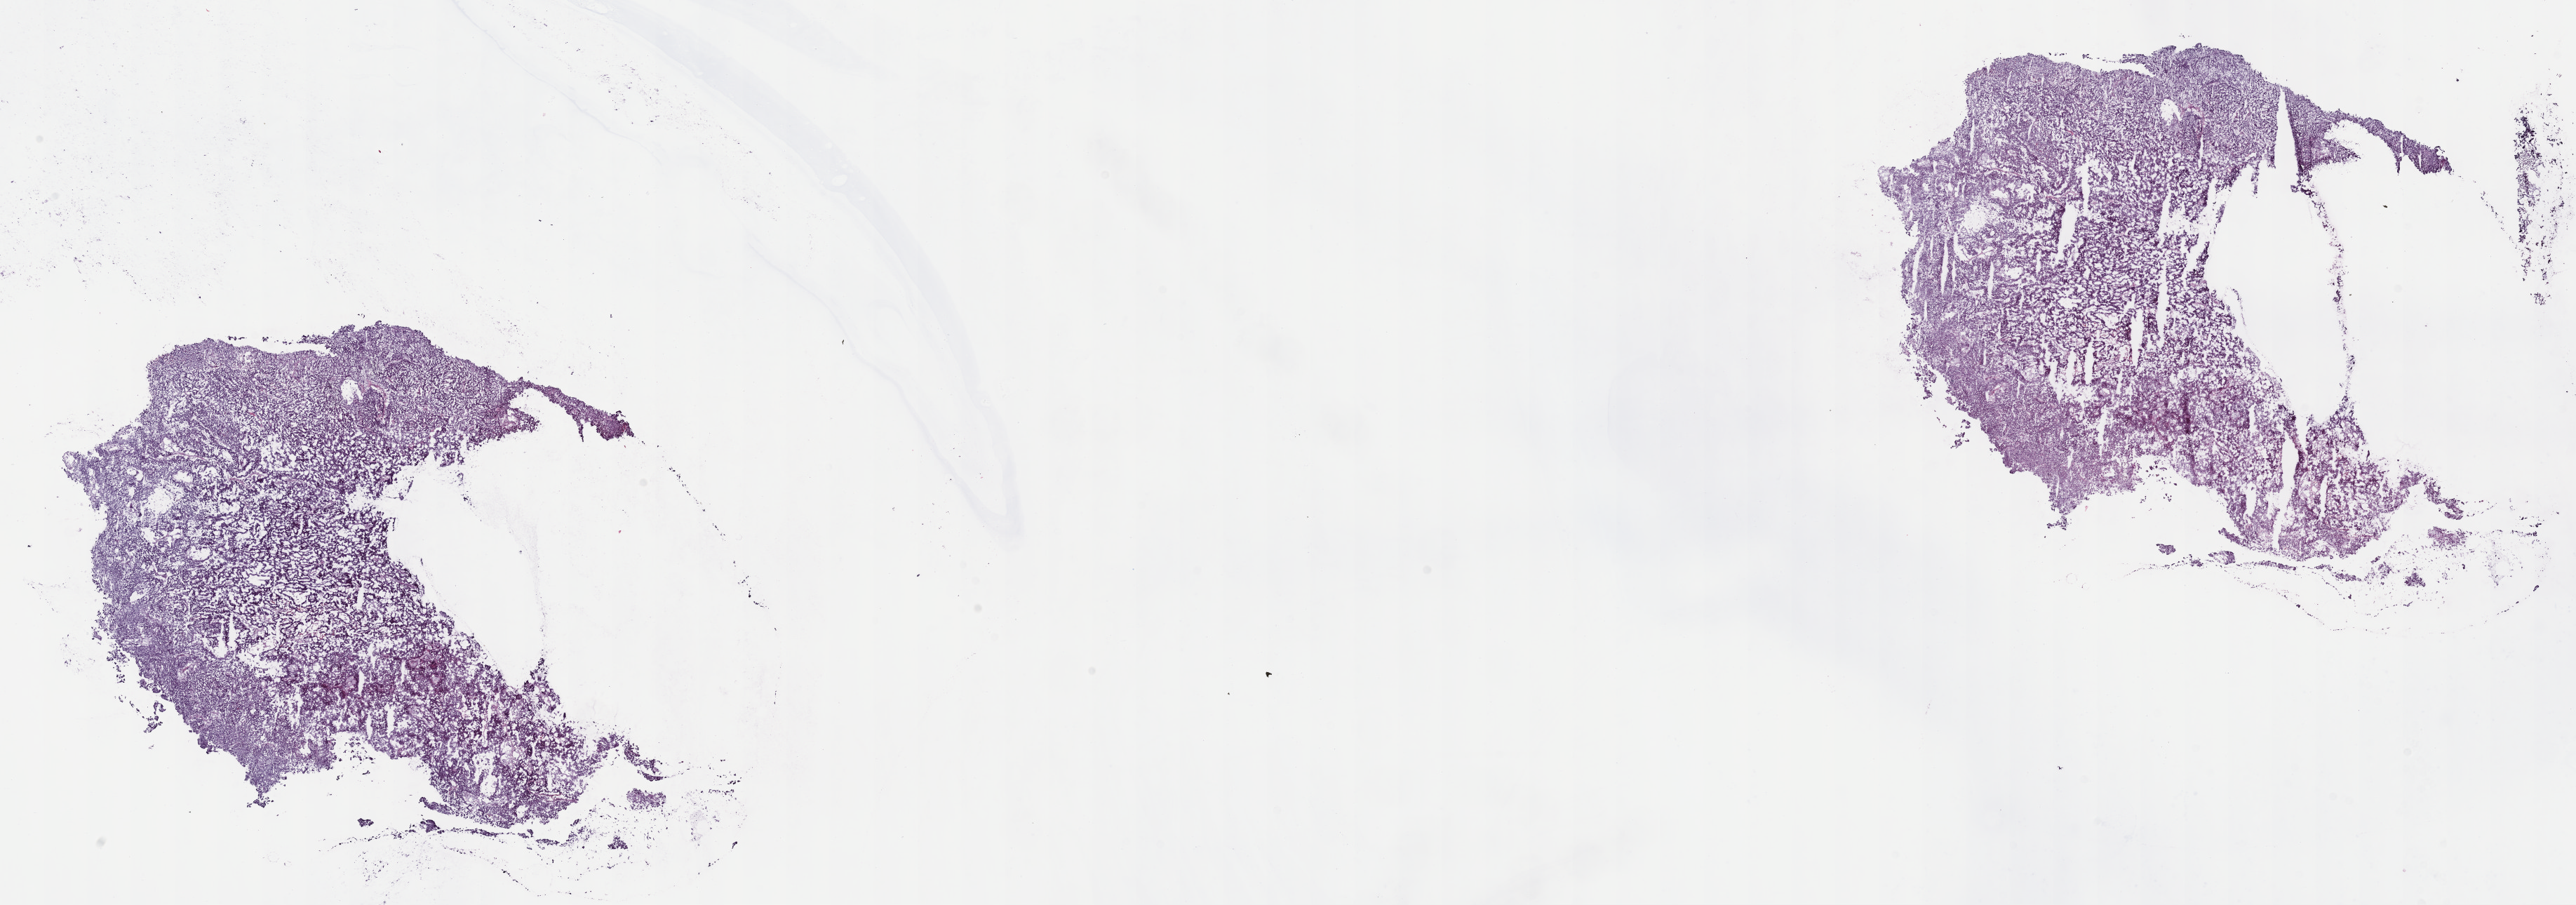
Digitized H&E-stained tissue section (whole slide) — whole scanned area (about 29.7 x 10.4 mm, acquisition: 40x scan) shown as a low-resolution overview; frozen section from the top of the tissue portion; primary tumour sample from the kidney. Patient: male, age at initial diagnosis 69 years. Composition of this section per pathologist review: tumour cells 70%, tumour nuclei 70%, normal cells 0%, stromal cells 25%, necrosis 5%. Infiltration values recorded for this section: lymphocyte infiltration 3%, monocyte infiltration 6%, neutrophil infiltration 1%.
Laterality: left. AJCC pathologic stage: I. Histologic diagnosis: Papillary adenocarcinoma, NOS.